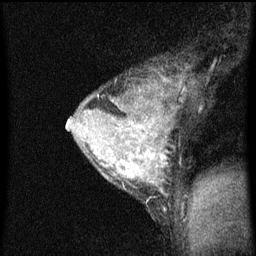
Breast MRI (dynamic contrast-enhanced), one sagittal slice; slice 46 of 60 in the series (ordered by position); dynamic contrast-enhanced series, image 2 of 3 at this slice position (ordered by acquisition); 1.5 T; TE 4.2 ms, TR 8 ms; 2 mm slice thickness; 256 × 256 image matrix, field of view 180 × 180 mm. Patient: female, 33 years.
Outlined on this slice (semi-automatic segmentation, software-assisted and operator-edited):
- analysis volume of interest (the breast-tissue region the enhancement analysis was run in; not a lesion): bounding box (x1, y1, x2, y2) in pixels: (66, 72, 190, 213)
- tumour enhancement mask (voxels above the 70 % enhancement threshold inside the analysis volume of interest): (68, 86, 166, 185)